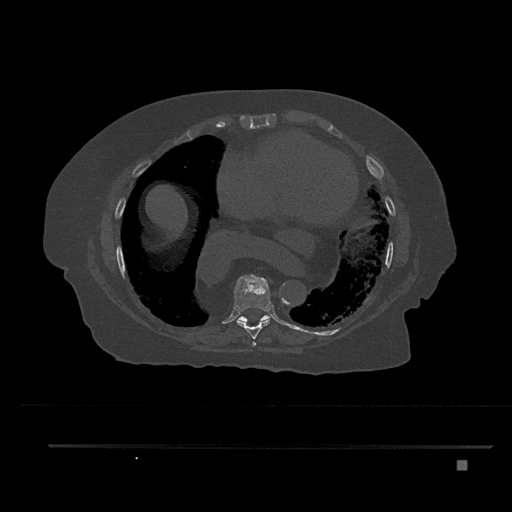
CT including the spine, one axial slice. Slice 429 of 797 in the series (ordered by position). Reconstruction kernel Br40s/3. Bone window (W 1800 / L 400 HU). 512 × 512 image matrix, field of view 437 × 437 mm. Patient: female, 76 years. From the clinical record (not read from this slice): primary cancer: lung; vertebrae with lytic lesions (as recorded): T11, L3.
Annotated regions visible in this slice (semi-automatic segmentation, software-assisted and operator-edited):
- T7 vertebra: bounding box <252,342,256,345> (left, top, right, bottom; pixels)
- T8 vertebra: <234,275,271,347>
- T9 vertebra: <237,311,271,322>